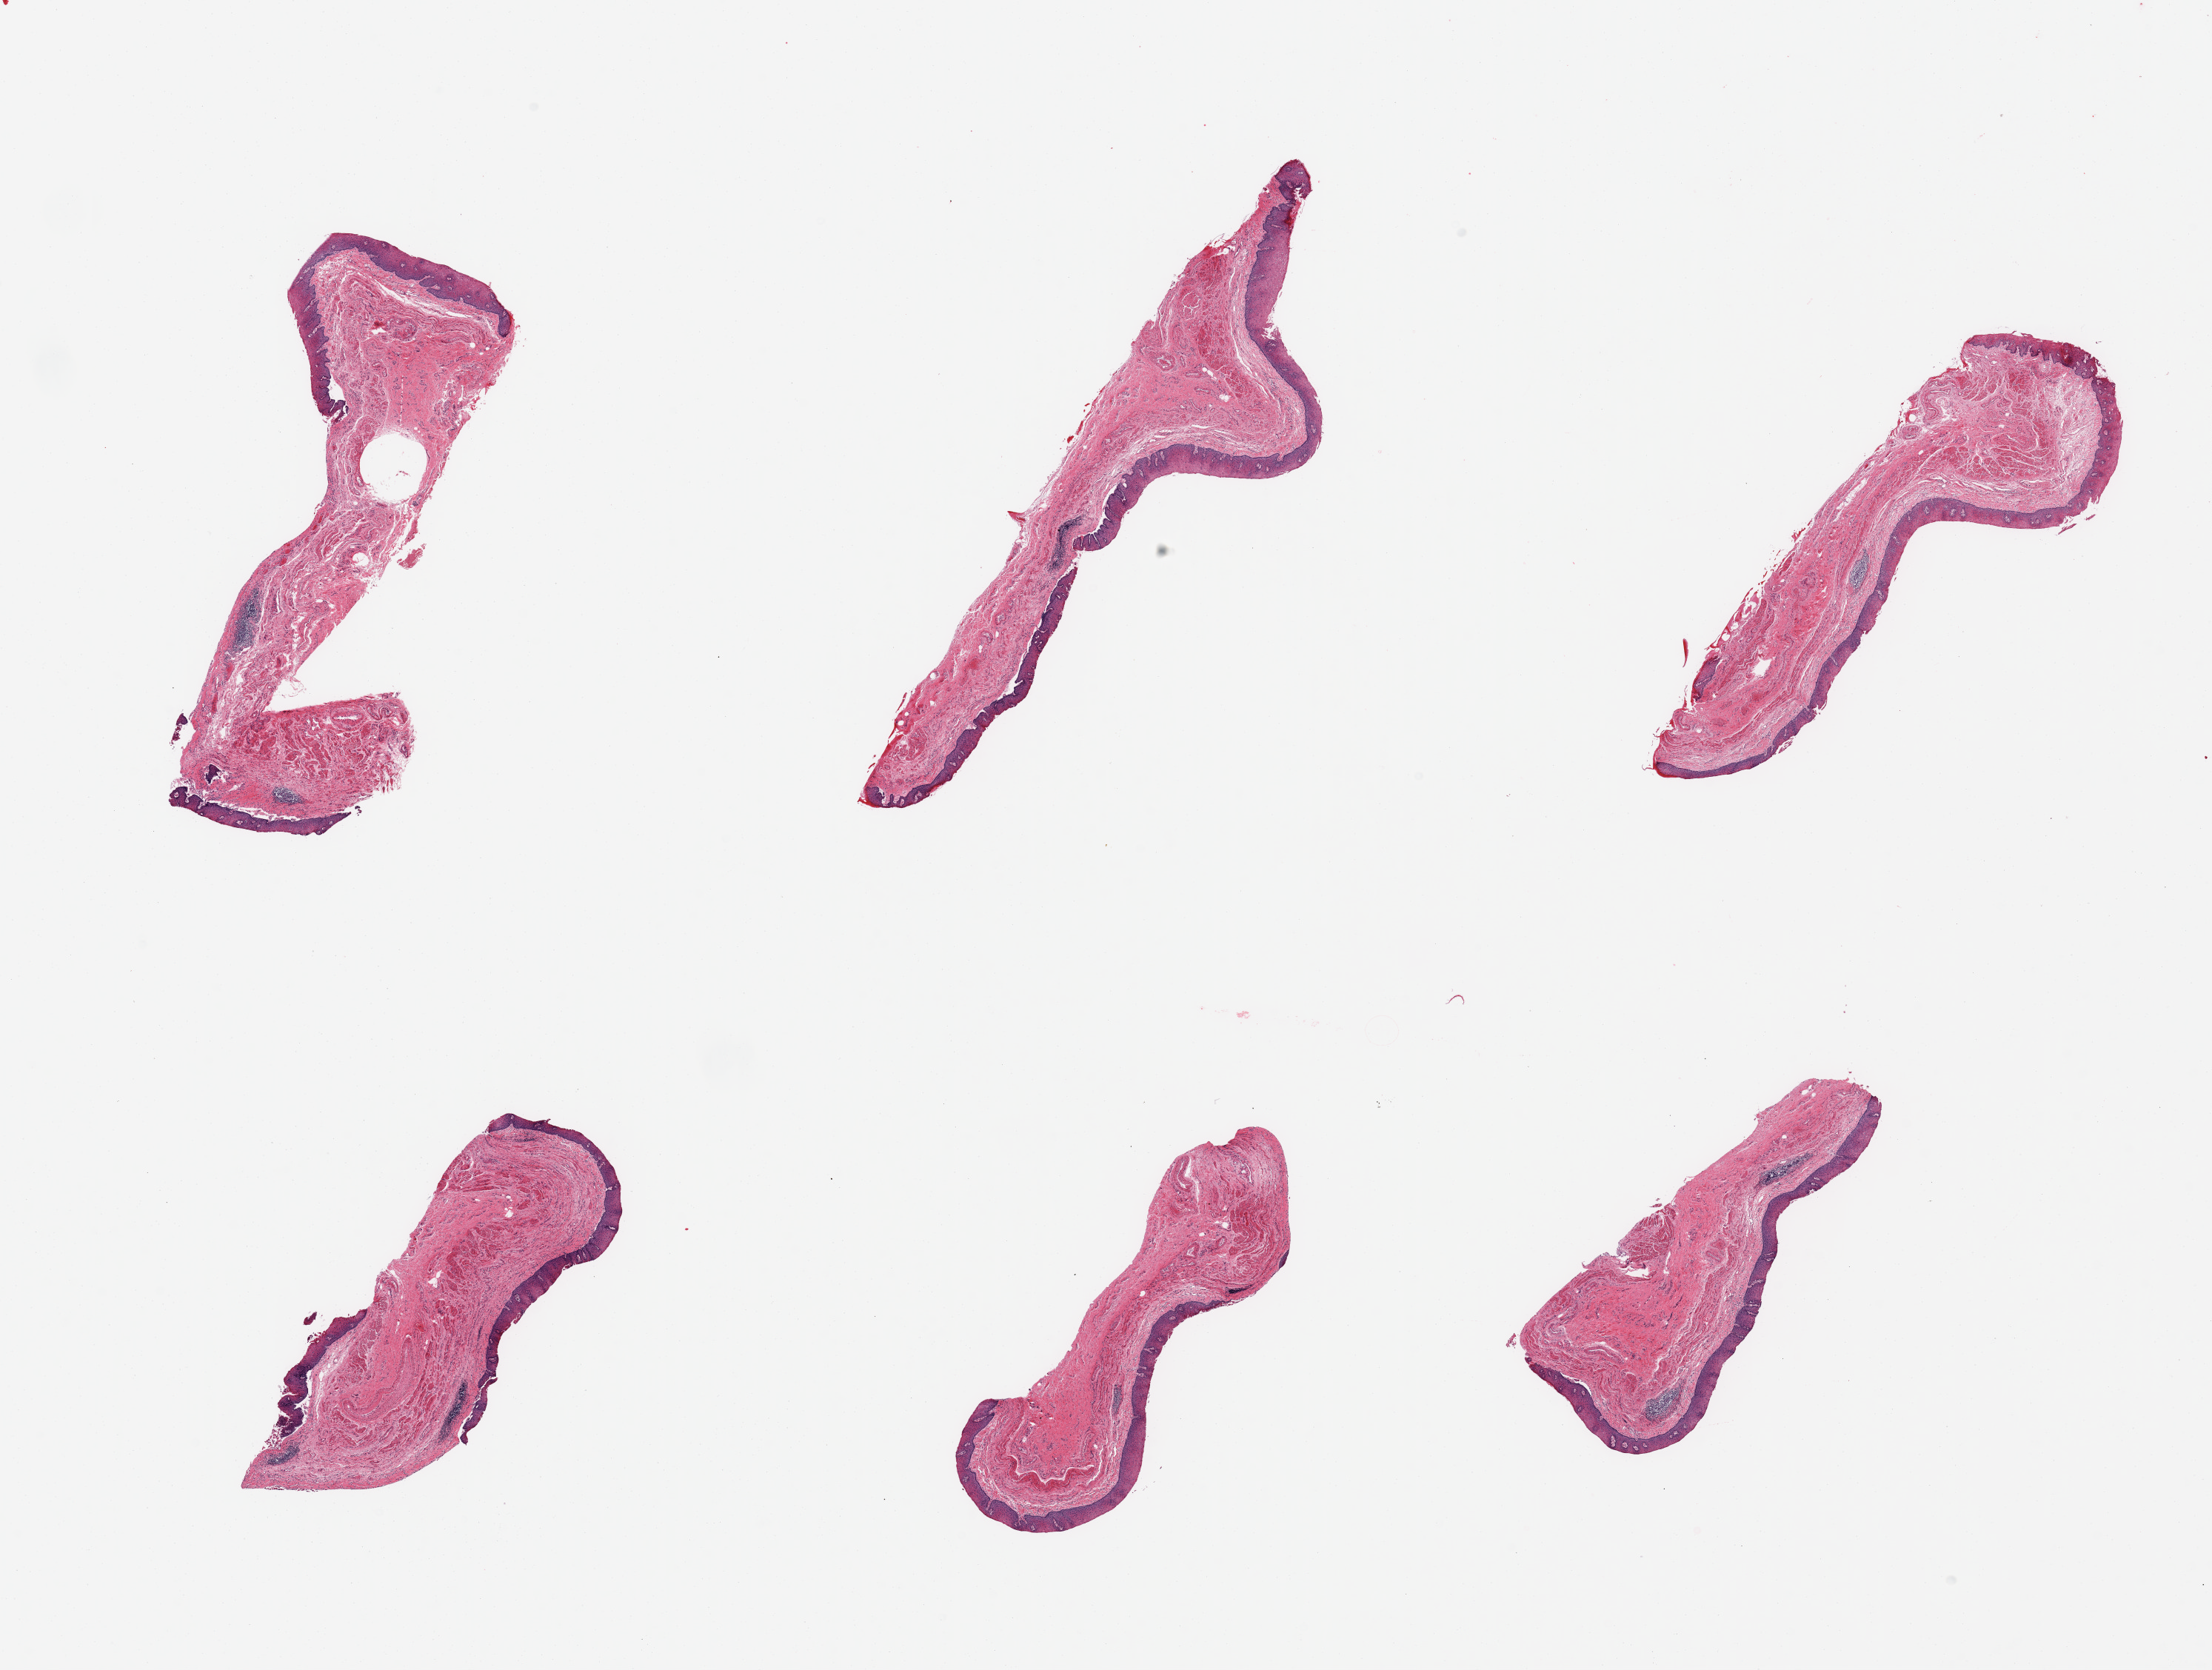
Digitized hematoxylin and eosin (H&E)-stained section, whole scanned area (about 23.6 x 17.8 mm) shown as a low-resolution overview, PAXgene-fixed paraffin-embedded (PFPE) section, section of esophageal mucous membrane (target tissue), tissue donor sample. Donor: male.
* review note (as recorded): 6 pieces. Squamous mucosa is ~0.1-0.2mm, ~10-20% thickness